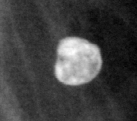
Crop from a digitized film mammogram around one marked abnormality, left breast, CC view, BI-RADS breast density category 1 (scale 1–4).
Calcifications, morphology lucent center; BI-RADS assessment category 2; benign; no additional work-up was recommended (benign without callback).